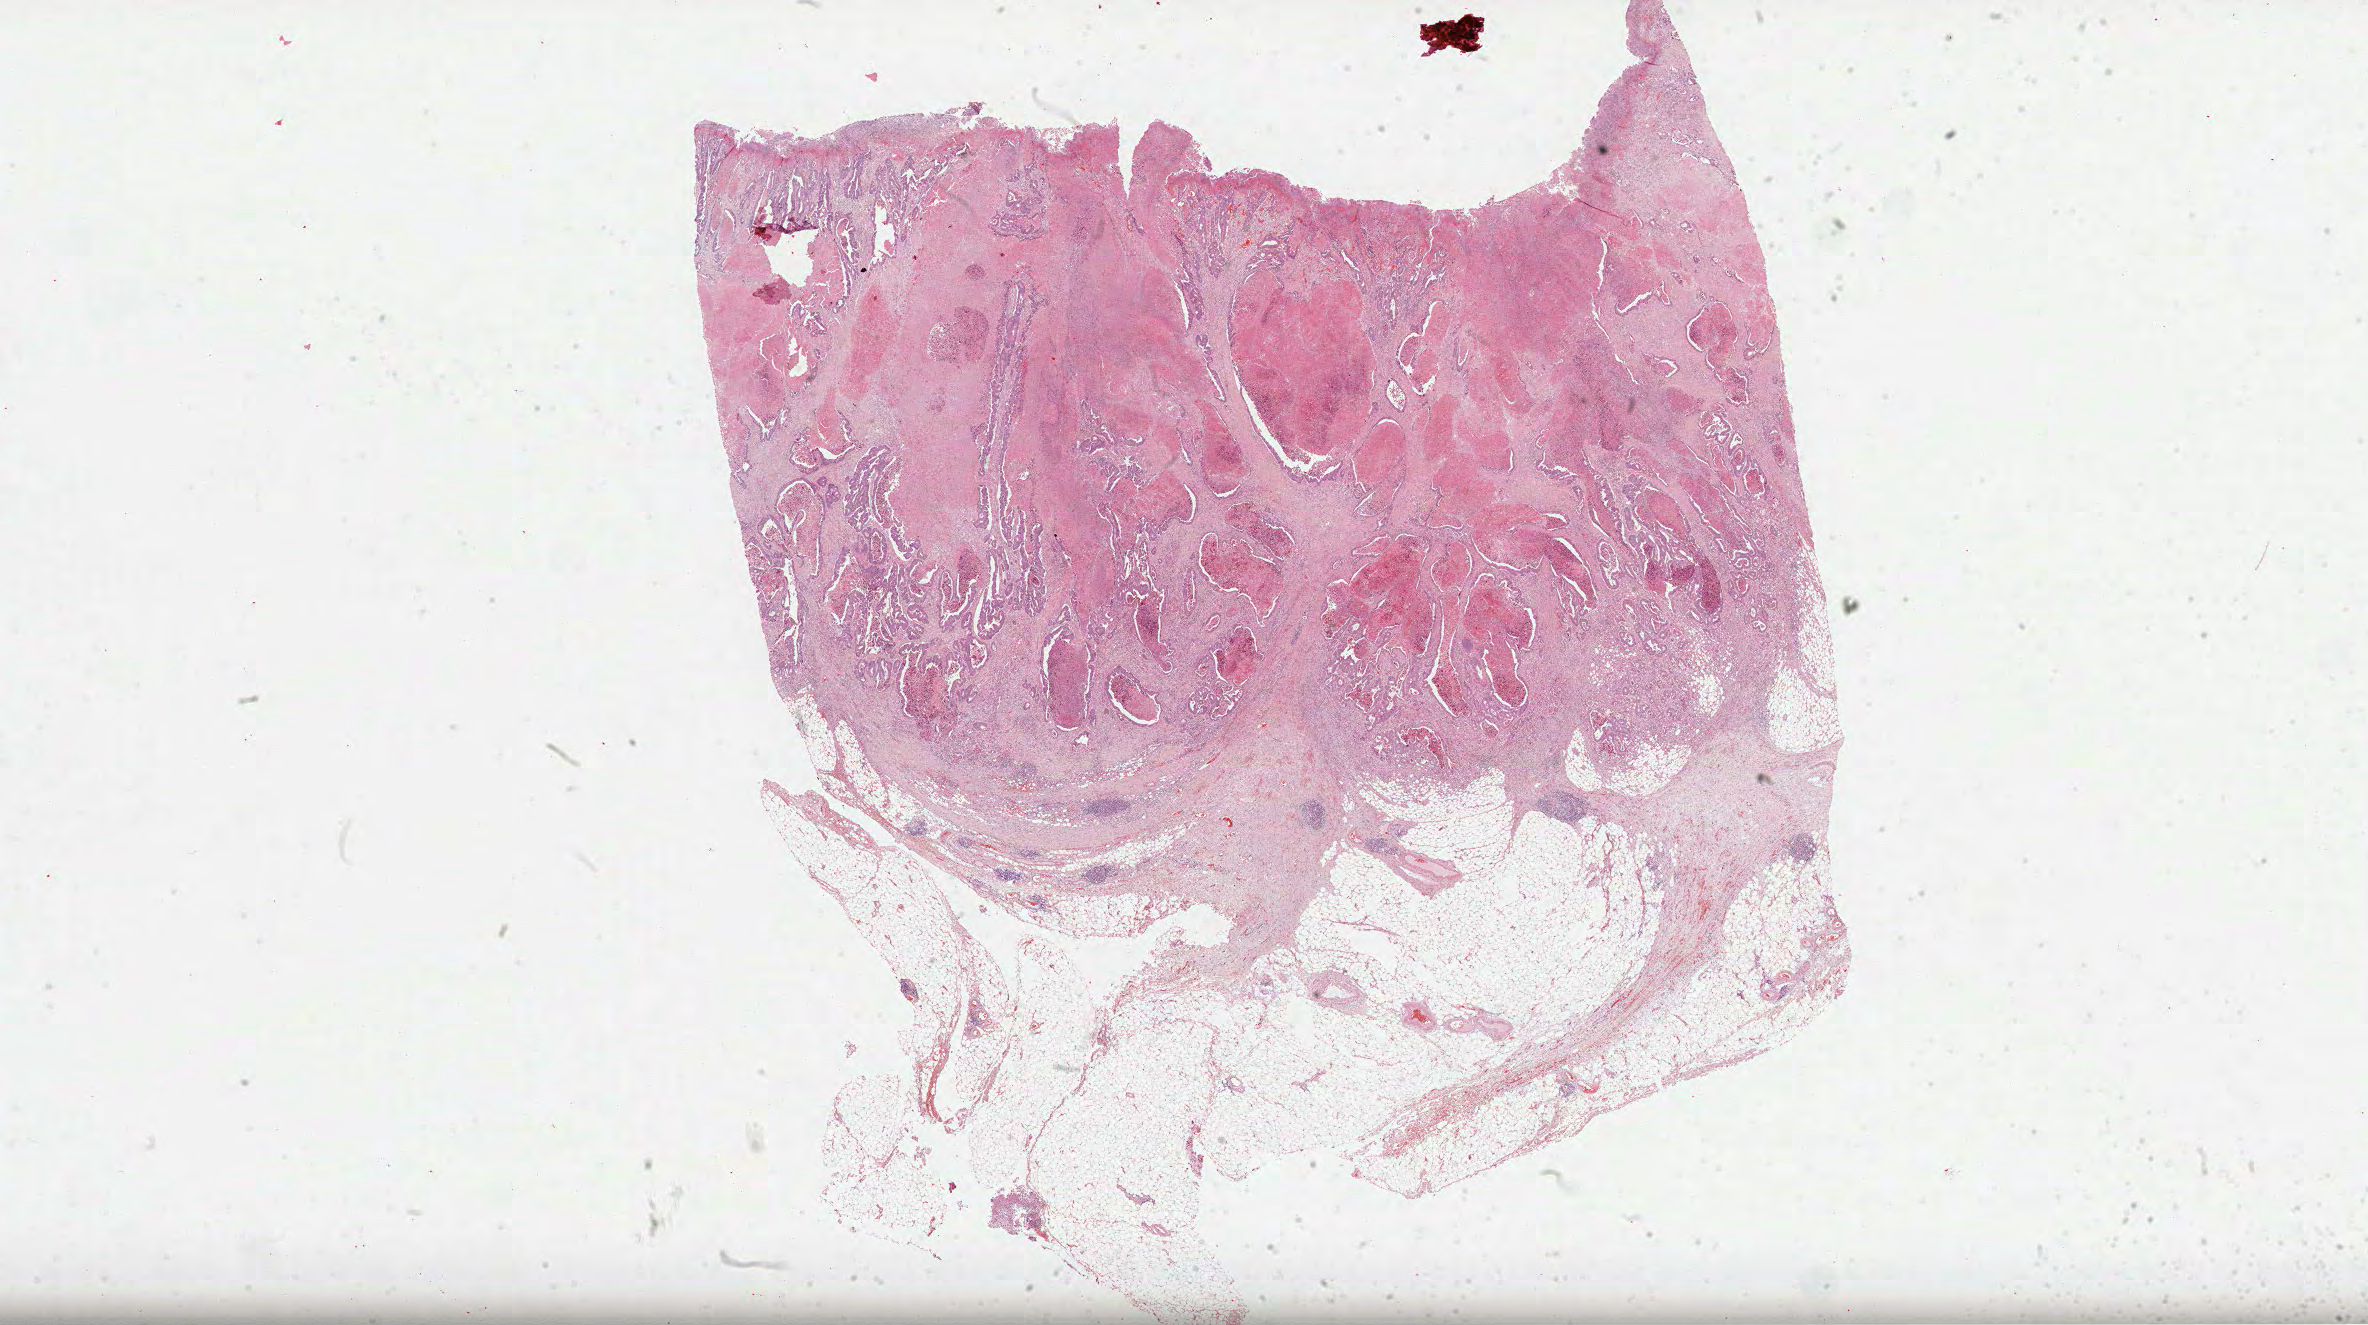
Whole-slide histology image, Hematoxylin and eosin (H&E) stained — a low-resolution overview of the entire scanned area, about 38.2 x 21.4 mm (slide scanned at 40x); FFPE section; colon, primary tumour sample. Female, age 80 years at initial diagnosis.
Lymph nodes positive (case pathology): 1 of 6 examined. AJCC pathologic stage: IIIB. Pathologic diagnosis: Adenocarcinoma, NOS.